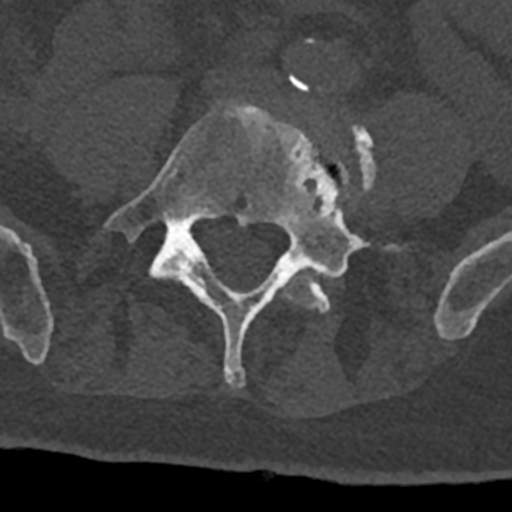
CT including the spine, one axial slice; position 211 of 797 along the scan axis; bone window (W 1800 / L 400 HU); 0.5 mm slice thickness; 512 × 512 image matrix, field of view 160 × 160 mm. Male patient, age 74 years. Case-level facts recorded for this patient, not image findings: primary cancer: renal; vertebrae with lytic lesions (as recorded): T10, L1, L2, L3, L4, L5.
Annotated regions visible in this slice (semi-automatically segmented with operator editing):
- L4 vertebra: box from (x=282, y=83) to (x=376, y=313) px
- L5 vertebra: (x=104, y=100)–(x=393, y=388)